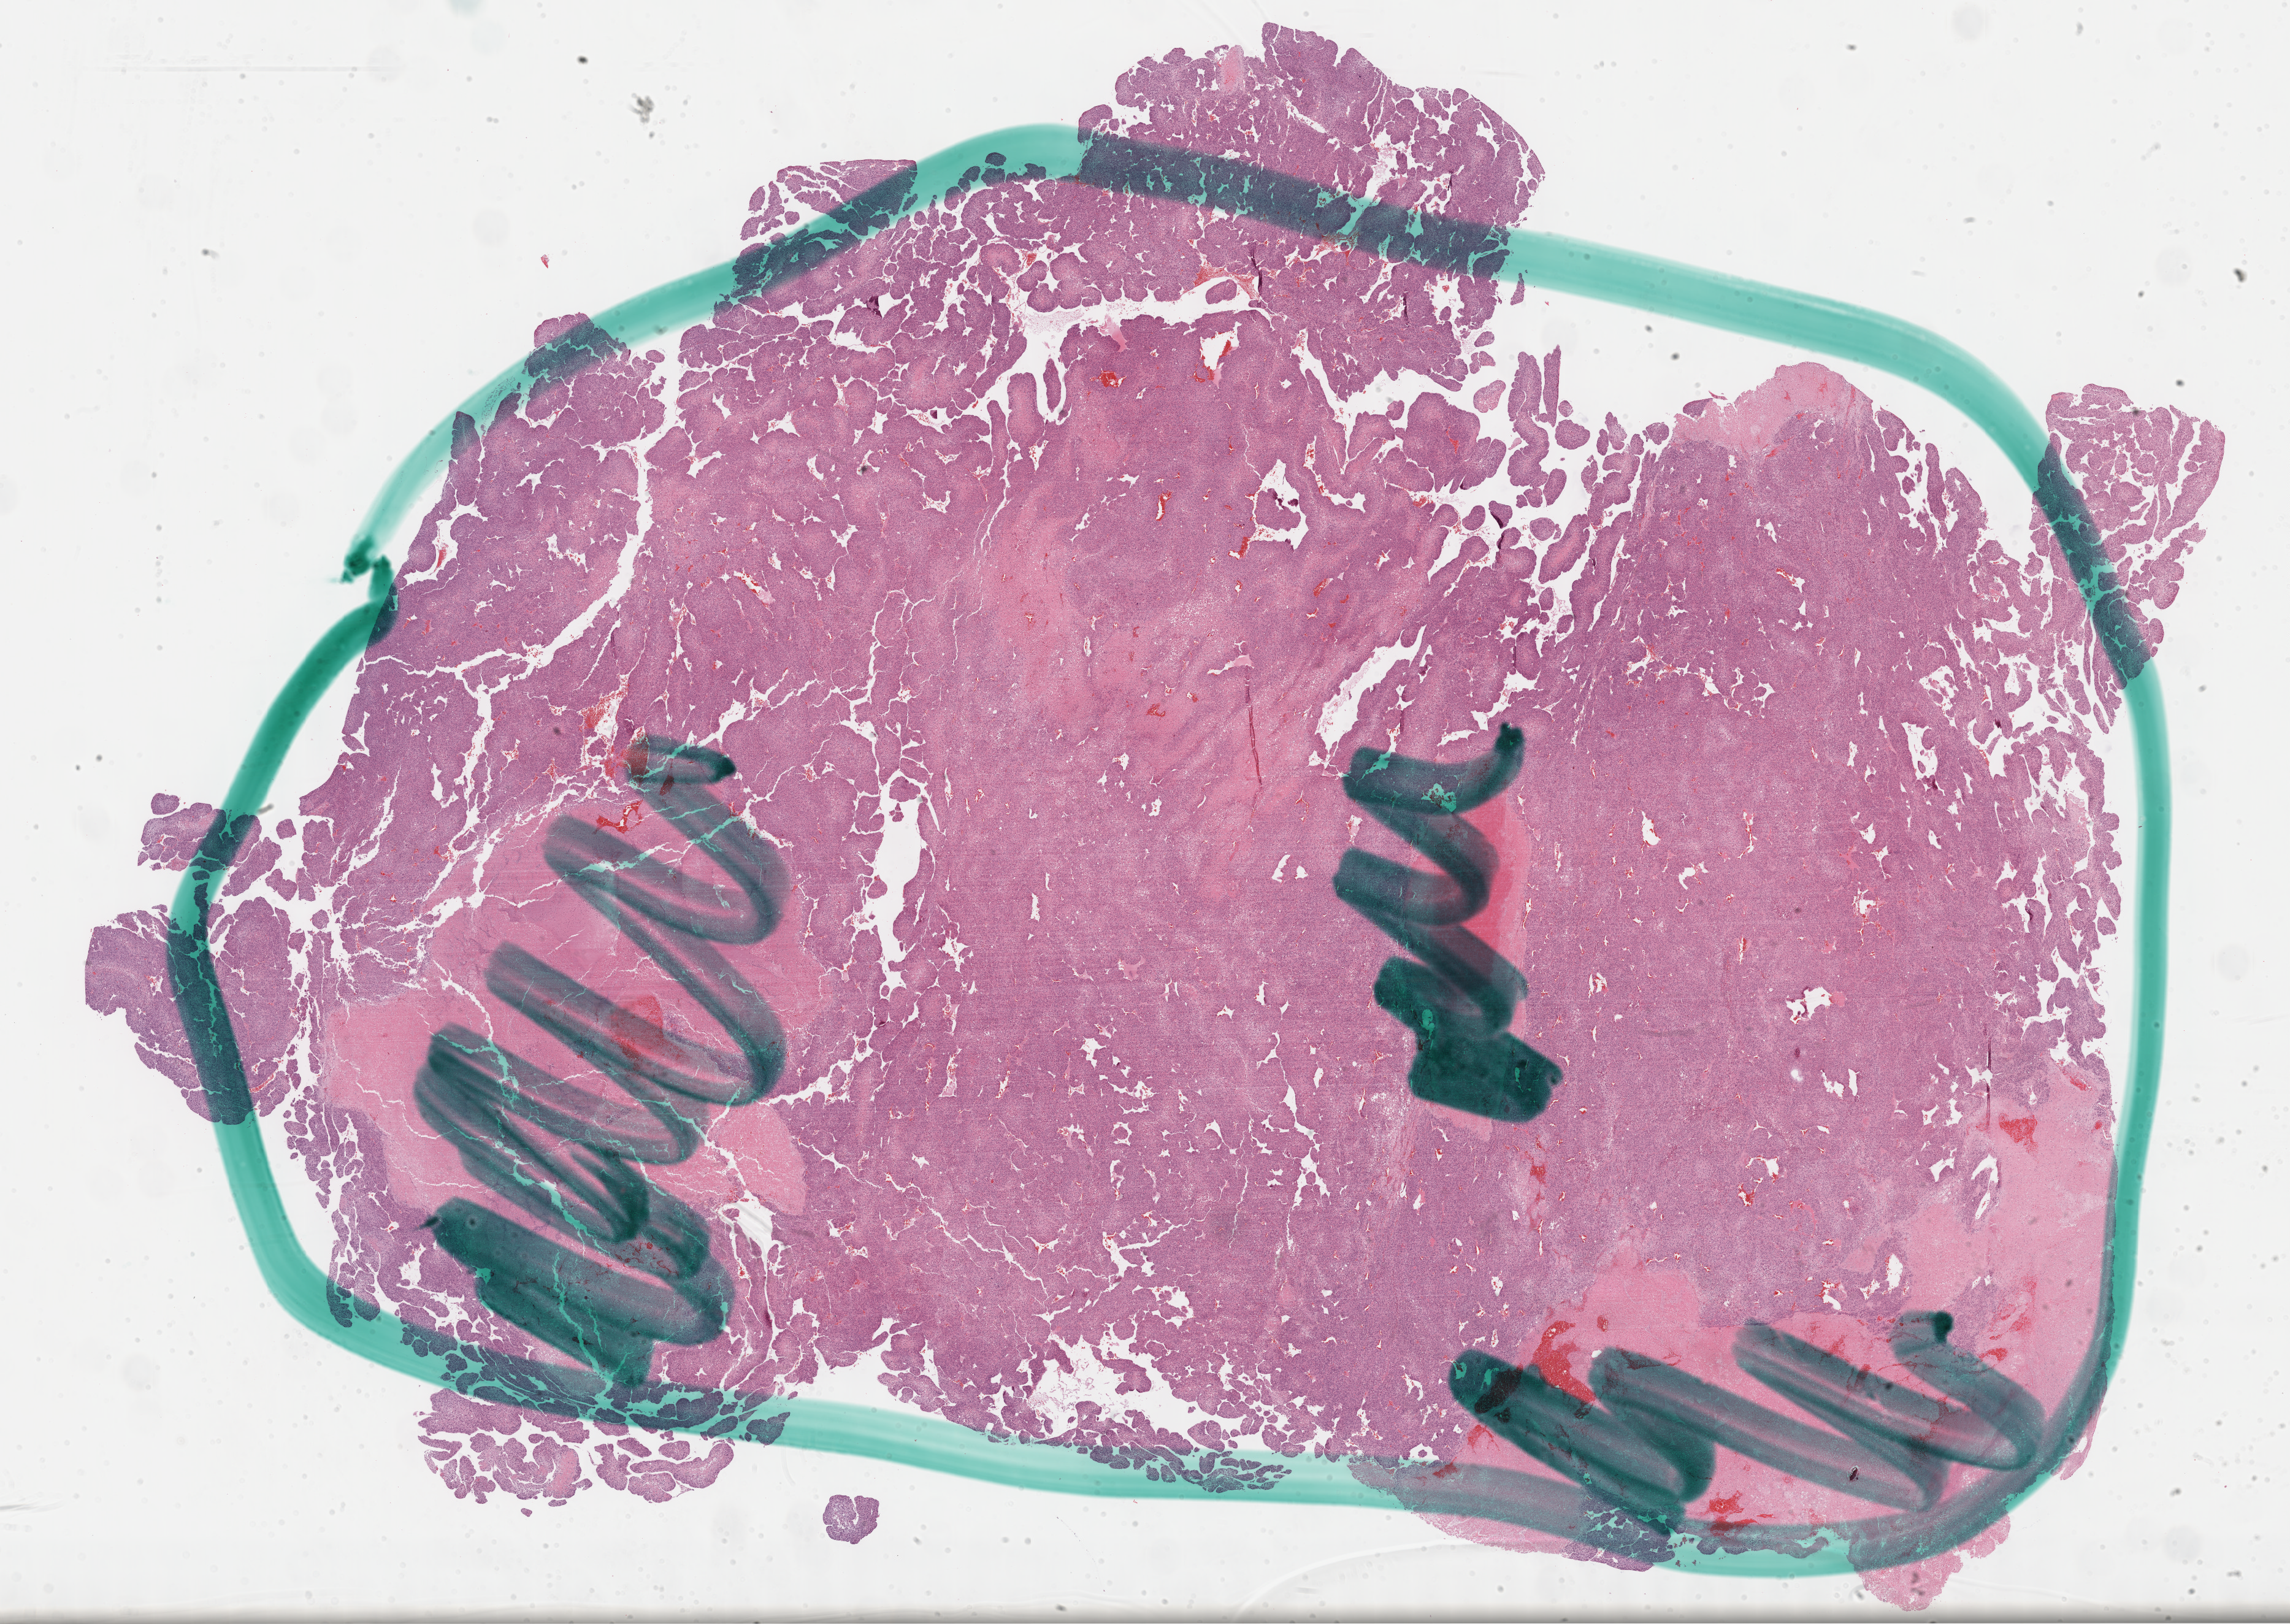
H&E whole-slide image — a low-resolution overview of the entire scanned area, about 30.2 x 21.4 mm. FFPE section. Adrenal cortex, primary tumour sample. Female patient; age at initial diagnosis 59 years.
Diagnosis: Adrenal cortical carcinoma. Lymph nodes positive (case pathology): 0 of 20 examined.